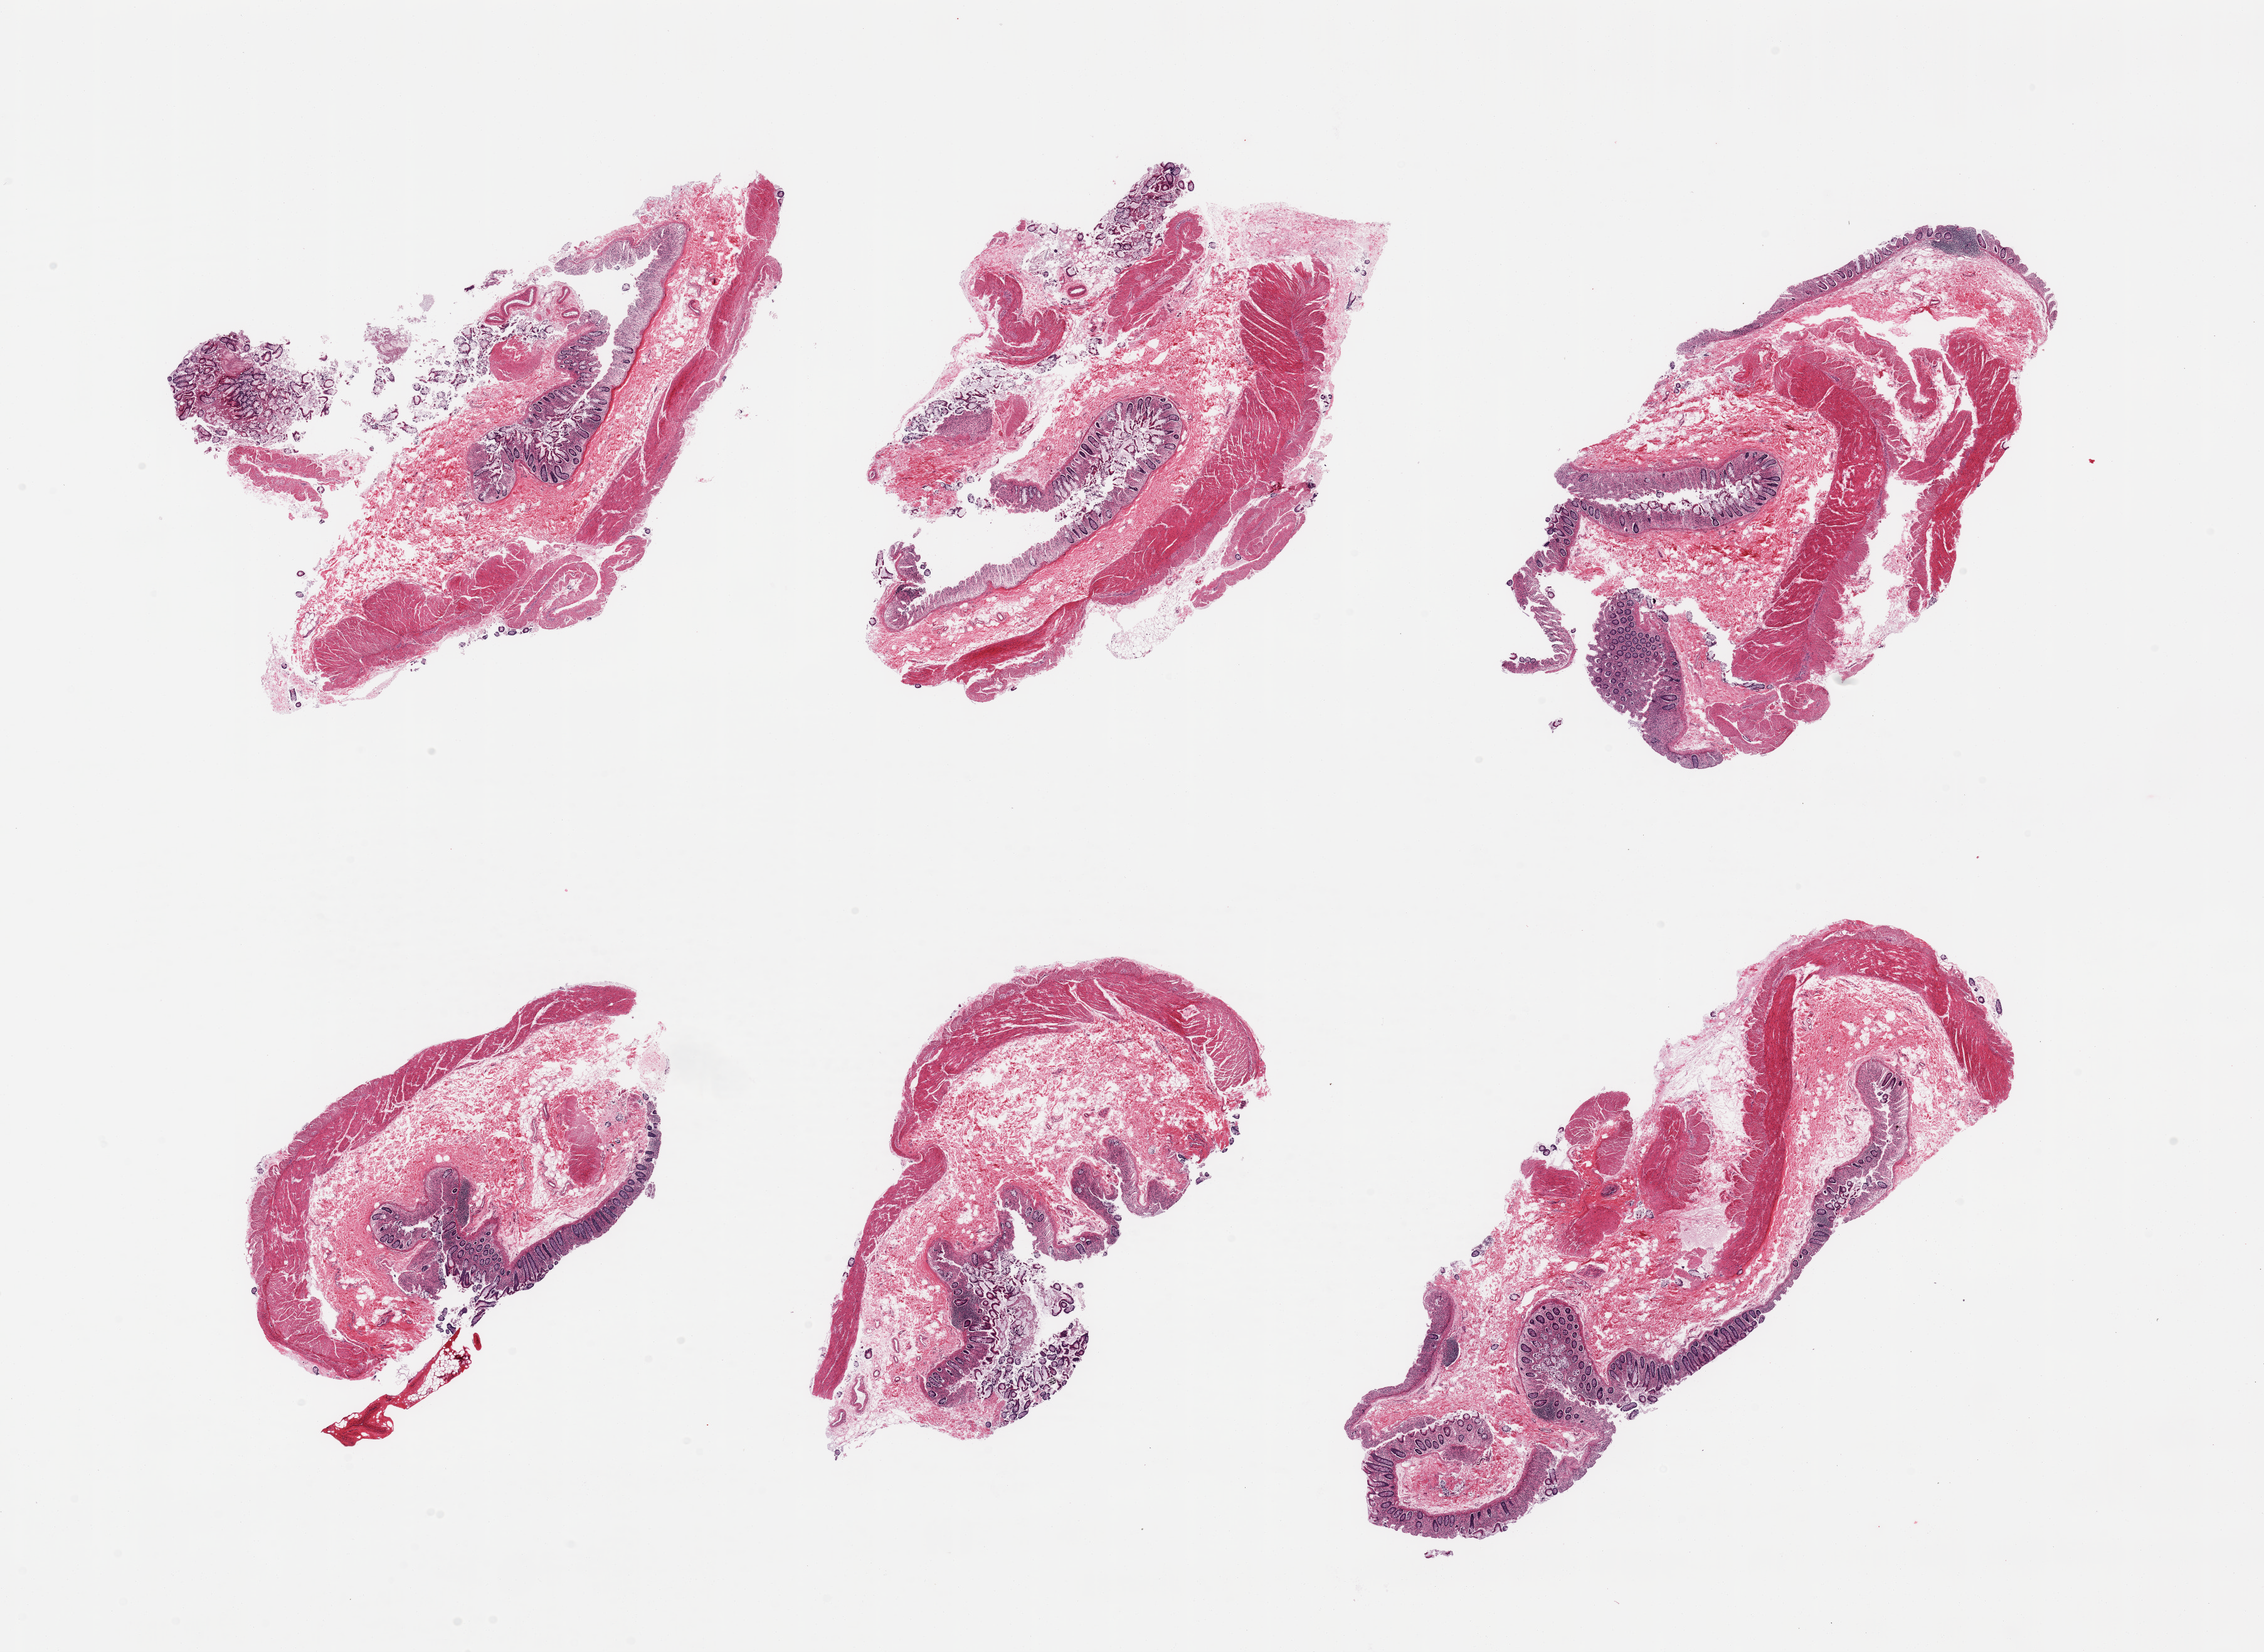
Digitized hematoxylin and eosin (H&E)-stained section, whole scanned area (about 28.5 x 20.8 mm) shown as a low-resolution overview, PAXgene-fixed, paraffin-embedded tissue, section of transverse colon (target tissue), donor tissue sample.
Review note (as recorded): 6 pieces; mucosa with variable states of autolysis.